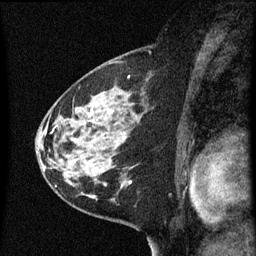
Breast MRI (dynamic contrast-enhanced), one sagittal slice; position 34 of 60 along the scan axis; dynamic contrast-enhanced series, image 2 of 3 at this slice position (ordered by acquisition); 1.5 T; TE 4.2 ms, TR 8 ms; 2 mm slice thickness; 256 × 256 image matrix, field of view 180 × 180 mm. Female patient, age 60 years.
Outlined on this slice (semi-automatically segmented with operator editing):
- analysis volume of interest (the breast-tissue region the enhancement analysis was run in; not a lesion): bounding box (x1, y1, x2, y2) in pixels: (48, 82, 149, 183)
- tumour enhancement mask (voxels above the 70 % enhancement threshold inside the analysis volume of interest): (92, 110, 132, 183)